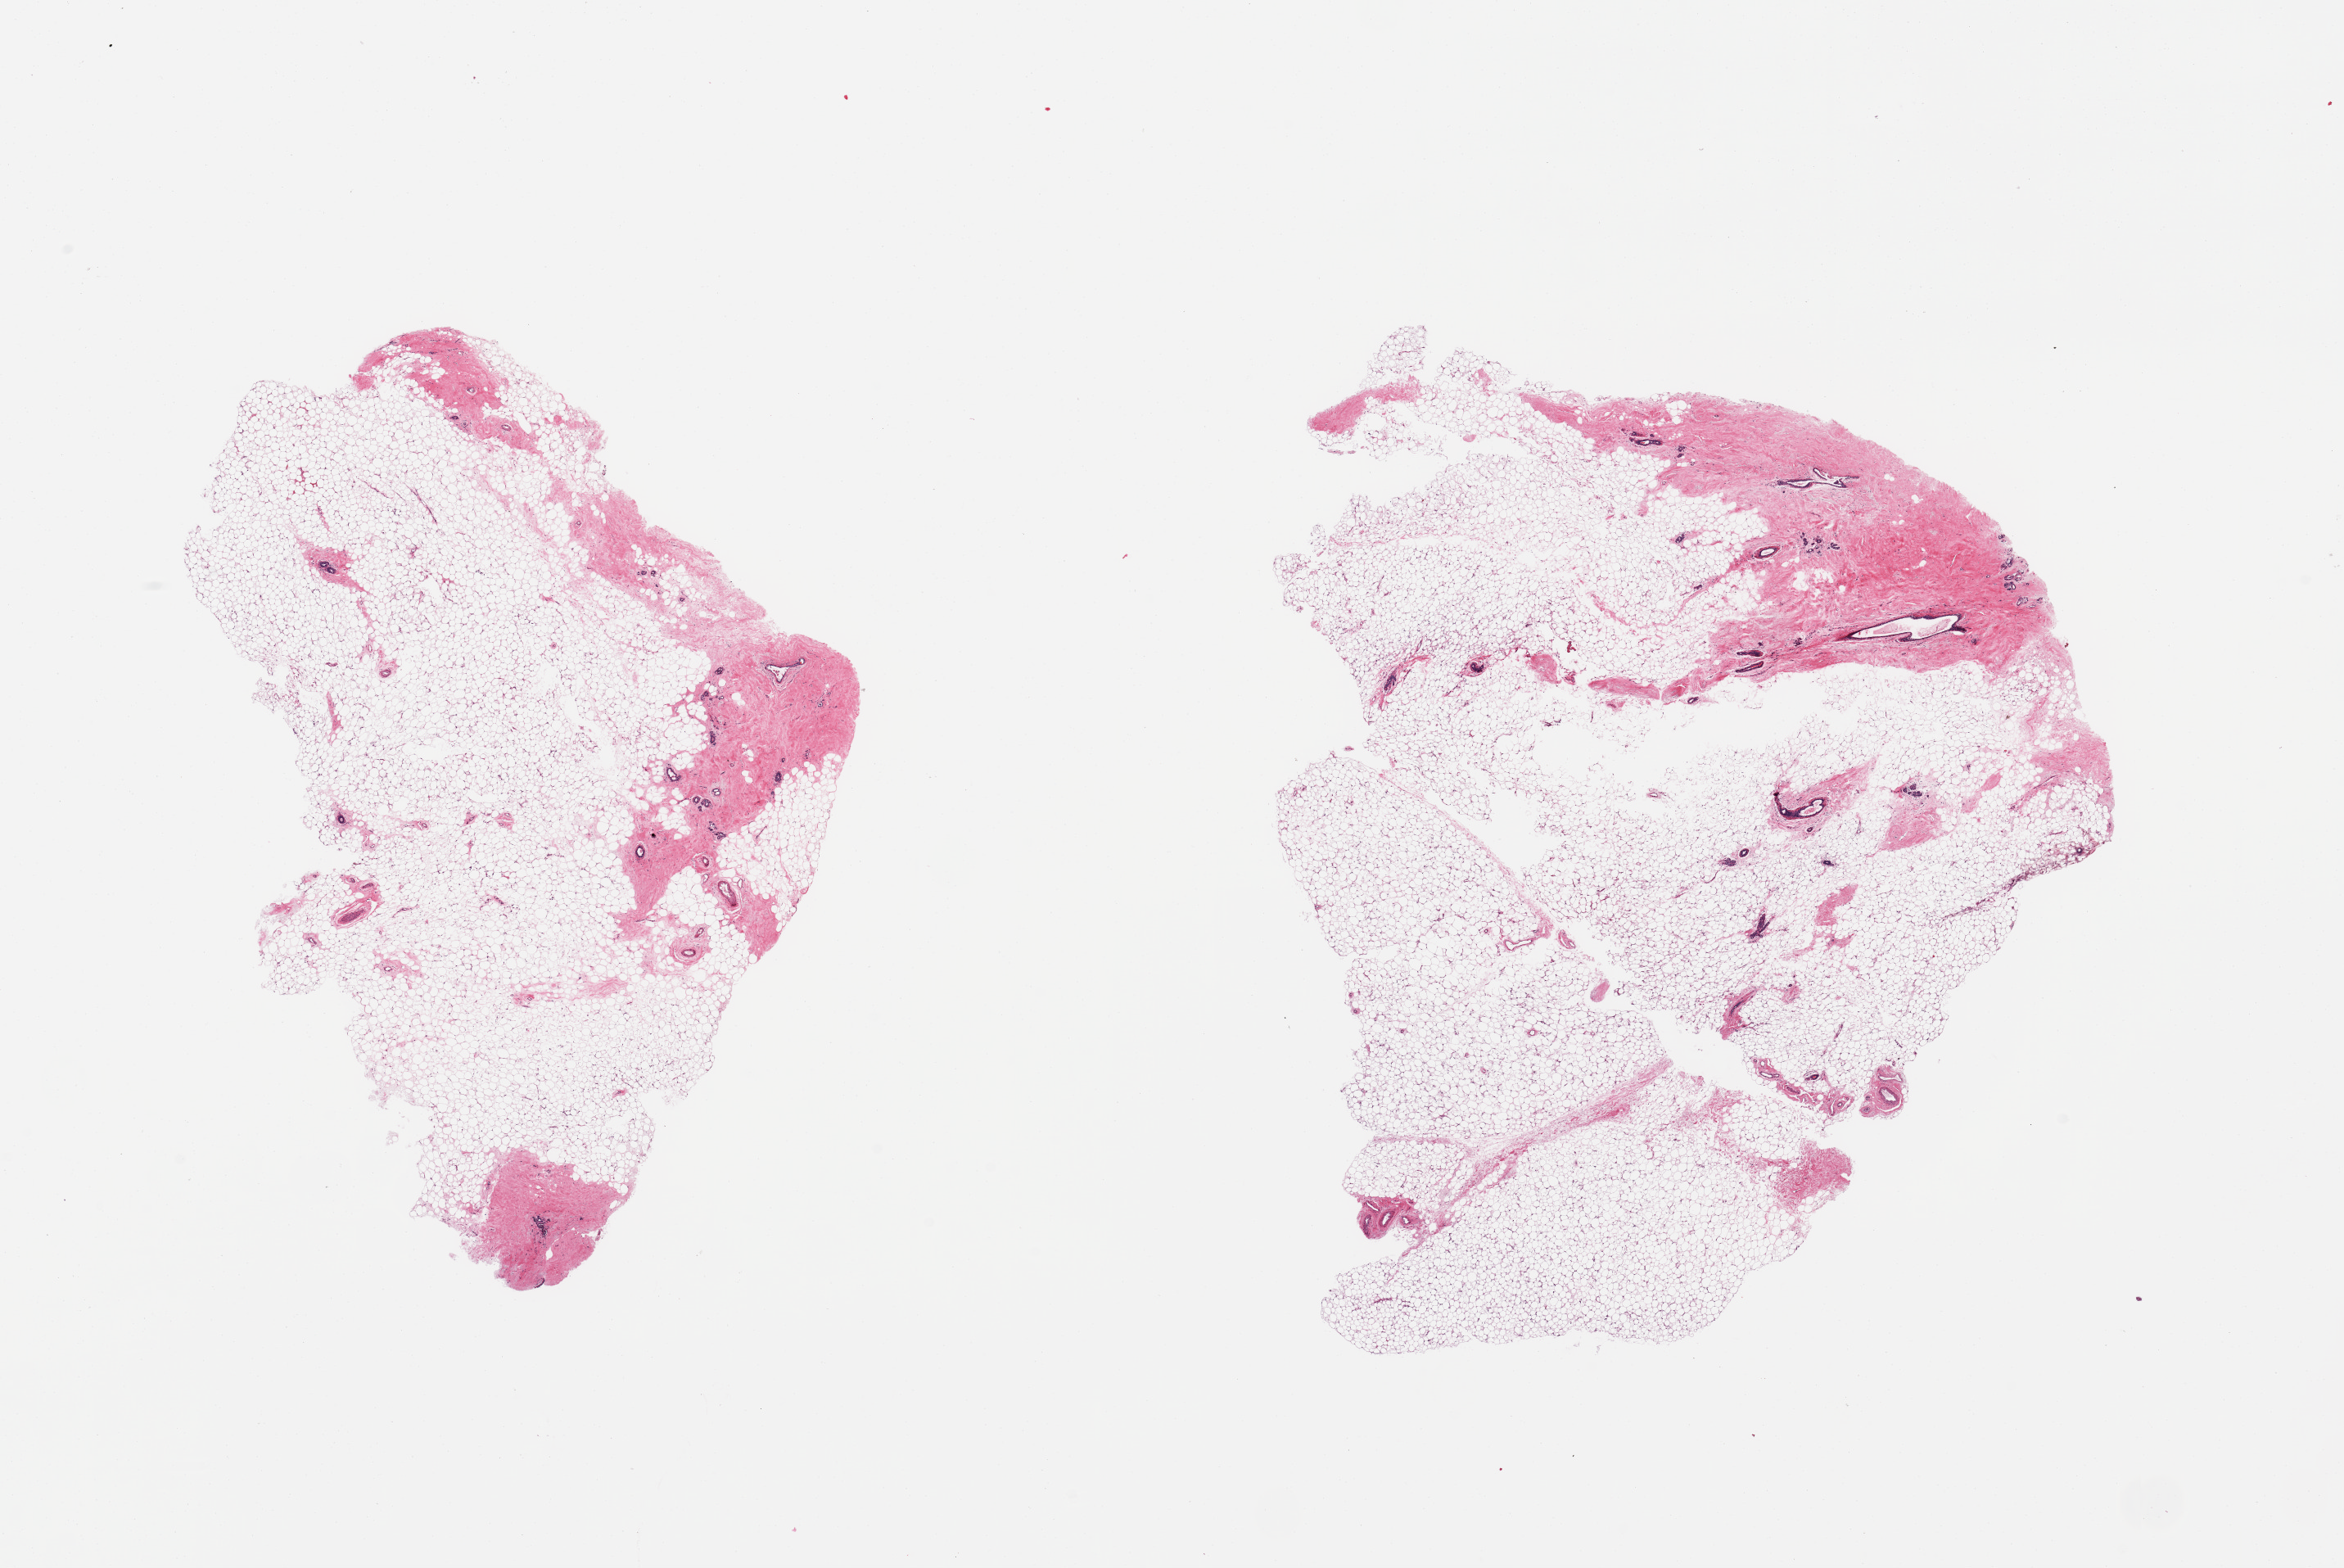
Whole-slide image, hematoxylin and eosin (H&E) stain, brightfield, whole scanned area (about 22.6 x 15.1 mm, slide scanned at 20x) shown as a low-resolution overview, PAXgene-fixed paraffin-embedded (PFPE) section, sampled site (target tissue): breast, tissue donor sample. Donor: female.
Review note (as recorded): 2 pieces; atrophic ductal and lobular units with 80% fat content.